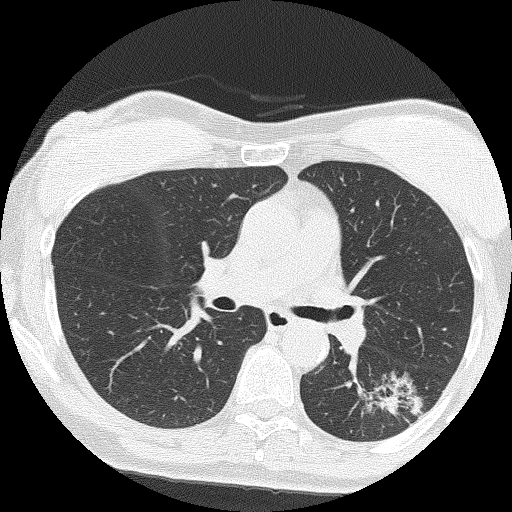
Axial slice from a low-dose chest CT screening exam. Second screening round (one year after baseline). Lung window (W 1500 / L -600 HU). 2 mm slice thickness. Lung (sharp) reconstruction kernel (FC51). 120 kVp. Slice 66 of 159 in the series. Female, age 64 years at enrolment. Former smoker at enrolment.
Expert reader's lesion annotation, bounding box (x1, y1, x2, y2) in pixels: (357, 372, 436, 439). The screening reader recorded 3 non-calcified nodules or masses ≥4 mm on this exam (right upper lobe, right upper lobe, right middle lobe); which of them this box marks is not recorded. Later outcome: lung cancer diagnosed 576 days after this screen — adenocarcinoma, NOS, left lower lobe, moderately differentiated (G2), stage IA (AJCC 6th edition), 17 mm at pathology.